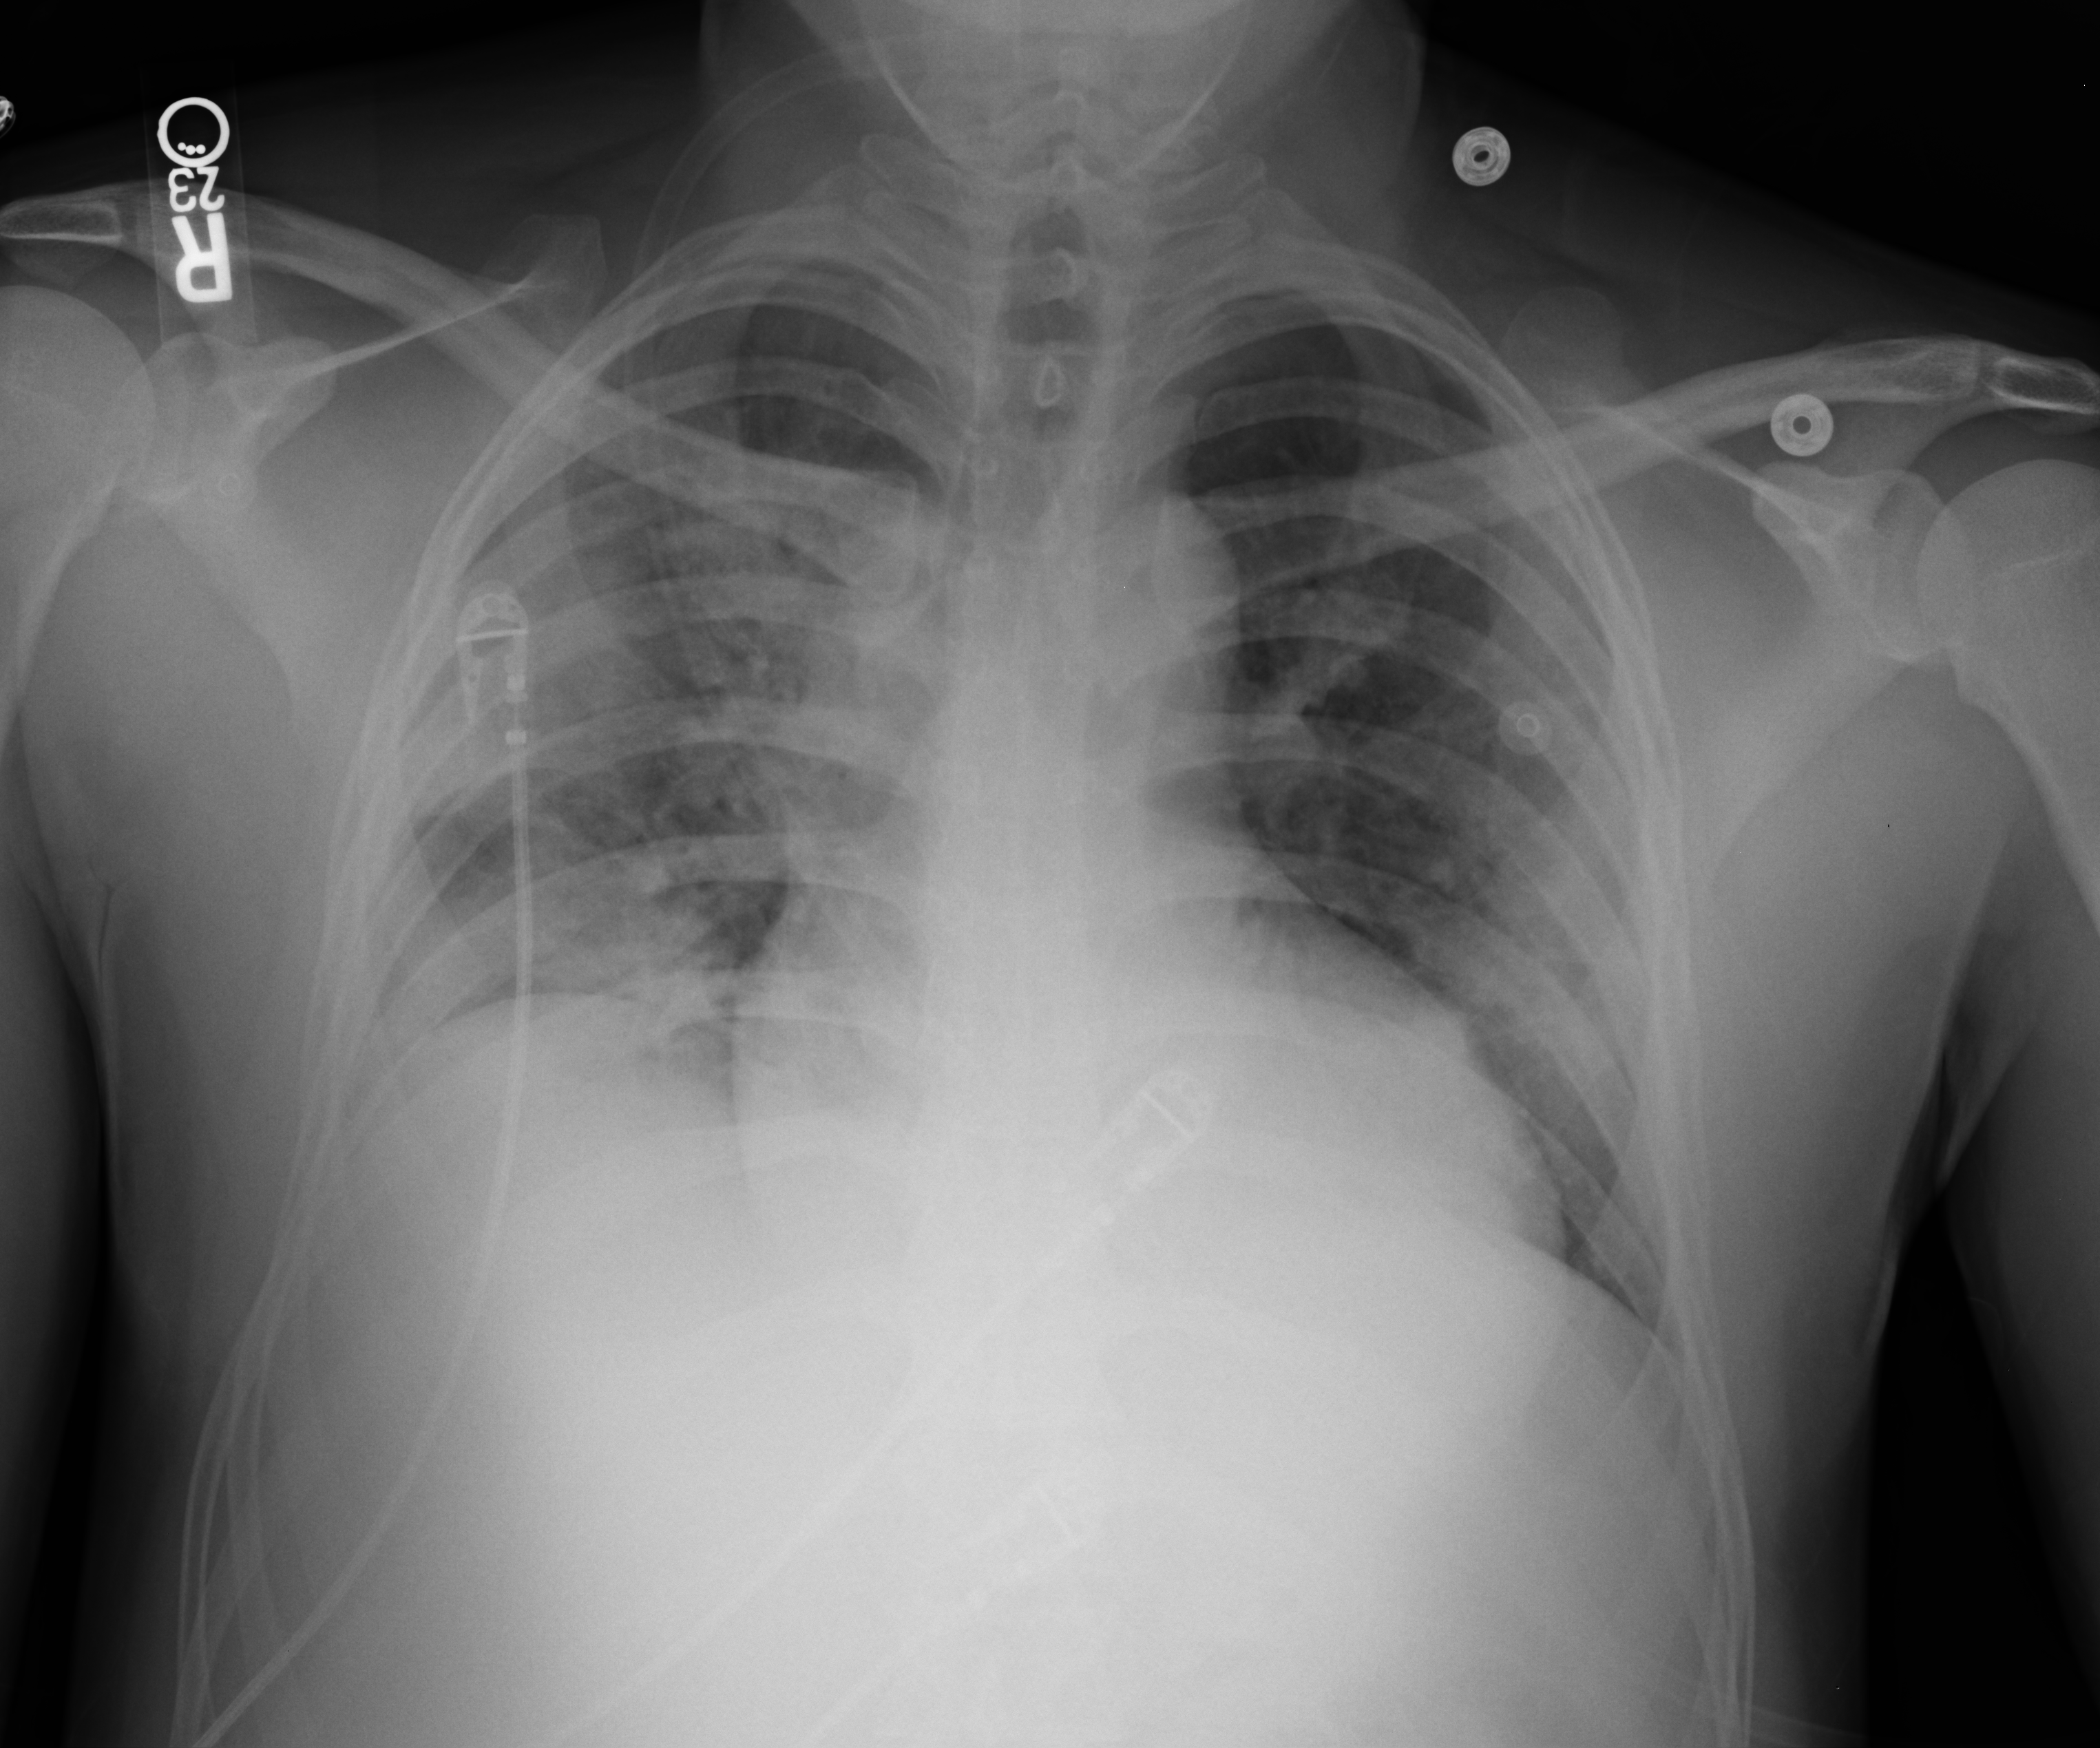
Bedside chest radiograph (computed radiography), anteroposterior (AP) projection. Patient hospitalised with COVID-19; male, aged 18–59 years.
From the hospital-stay record, not from the radiograph (when in the stay this image was taken is not recorded): length of hospital stay: 15 days; mechanically ventilated during this hospital stay: no.